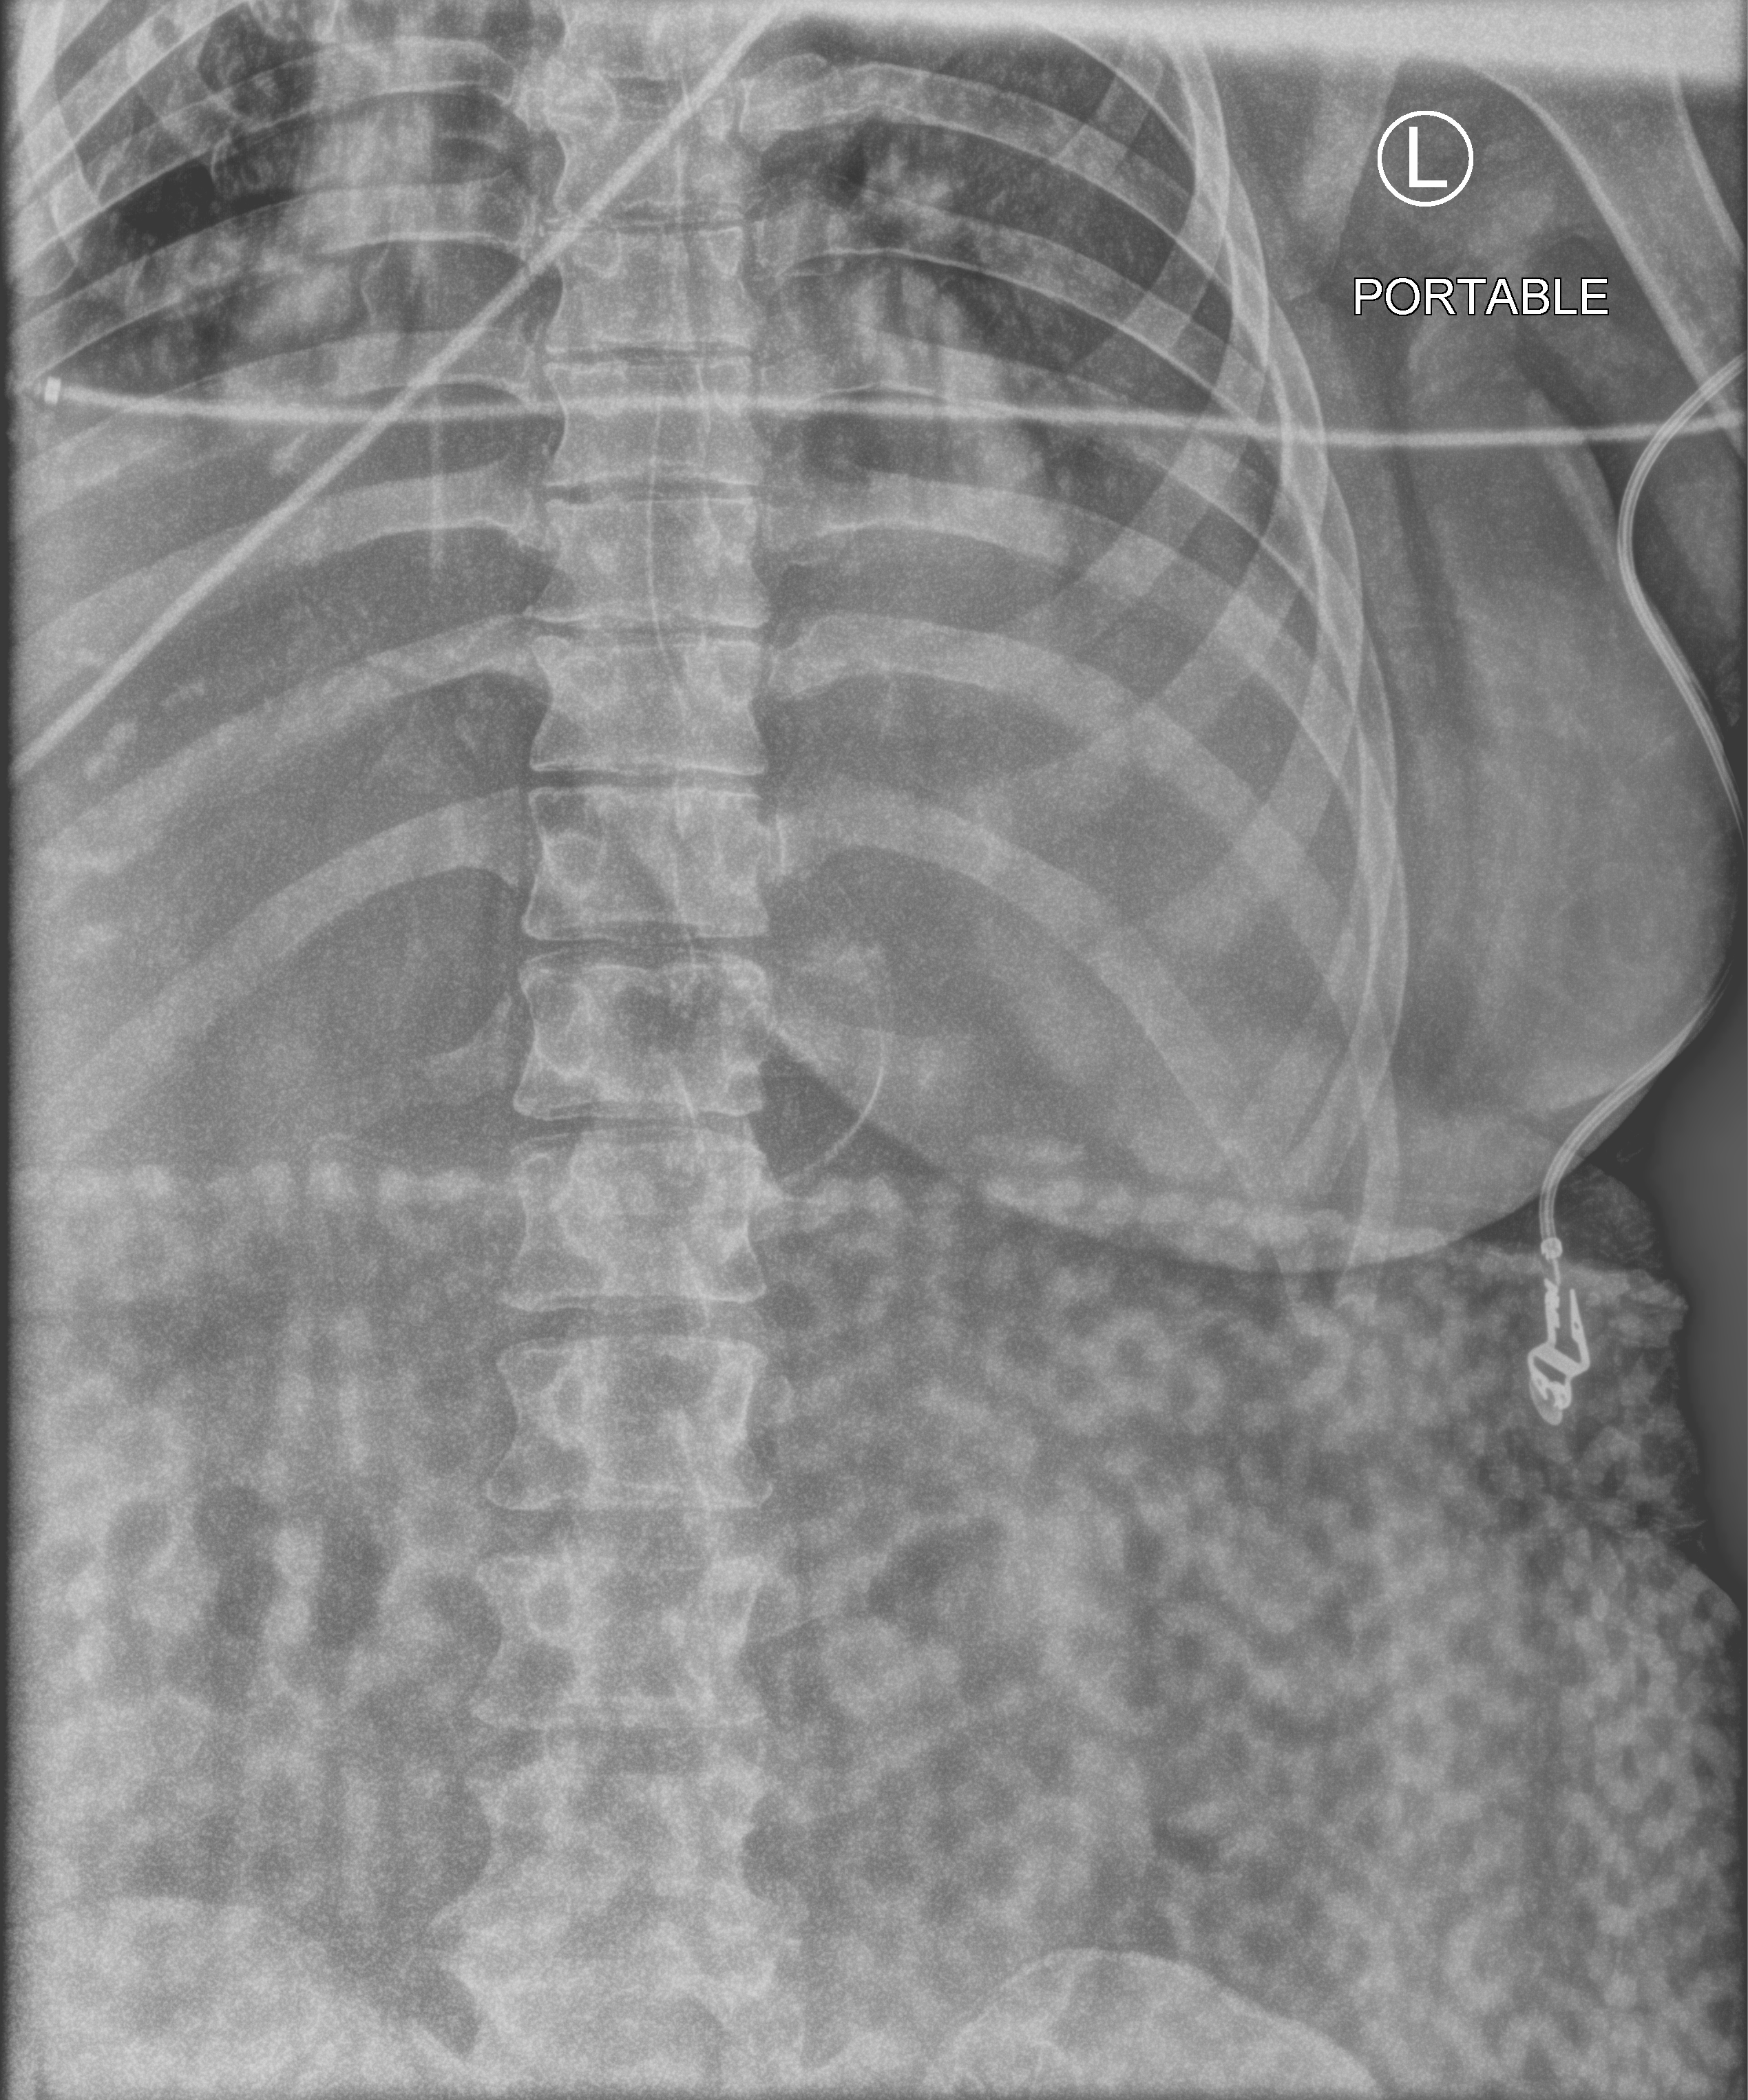
Portable abdomen radiograph, anteroposterior (AP) projection. Female patient hospitalised with COVID-19, age 18–59 years.
From the hospital-stay record, not from the radiograph (when in the stay this image was taken is not recorded): smoking status (admission record): never; mechanically ventilated during this hospital stay: yes.